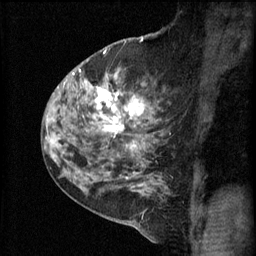
Breast MRI (dynamic contrast-enhanced), one sagittal slice. Slice 38 of 60 in the series (ordered by position). 3 images stored at this slice position (order not interpretable as contrast timing). 1.5 T. TE 4.2 ms, TR 11 ms. 2.3 mm slice thickness. 256 × 256 image matrix, field of view 180 × 180 mm. Patient: female, 52 years.
Annotated regions visible in this slice (semi-automatically segmented with operator editing):
- analysis volume of interest (the breast-tissue region the enhancement analysis was run in; not a lesion): bounding box (x1, y1, x2, y2) in pixels: (86, 76, 164, 157)
- tumour enhancement mask (voxels above the 70 % enhancement threshold inside the analysis volume of interest): (86, 82, 144, 153)